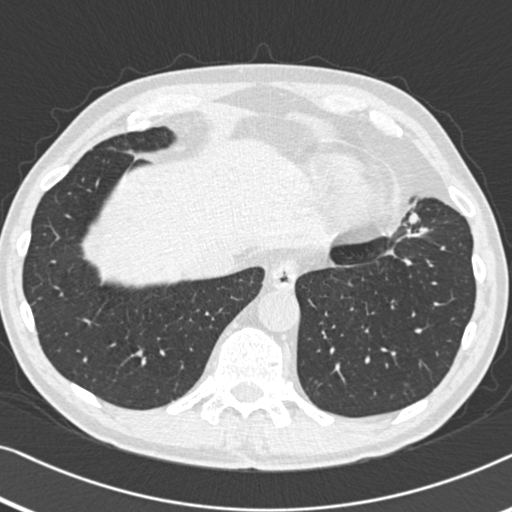
Low-dose screening chest CT, one axial slice. Position 118 of 383 along the scan axis. Reconstruction kernel B30f. 120 kVp. Lung window (W 1500 / L -600 HU). 1 mm slice thickness. 512 × 512 image matrix, field of view 332 × 332 mm.
Structures marked on this image (manually delineated by an expert):
- lesion 1 (tumor, upper lobe of left lung): bounding box [x1, y1, x2, y2] px = [409, 213, 419, 224]